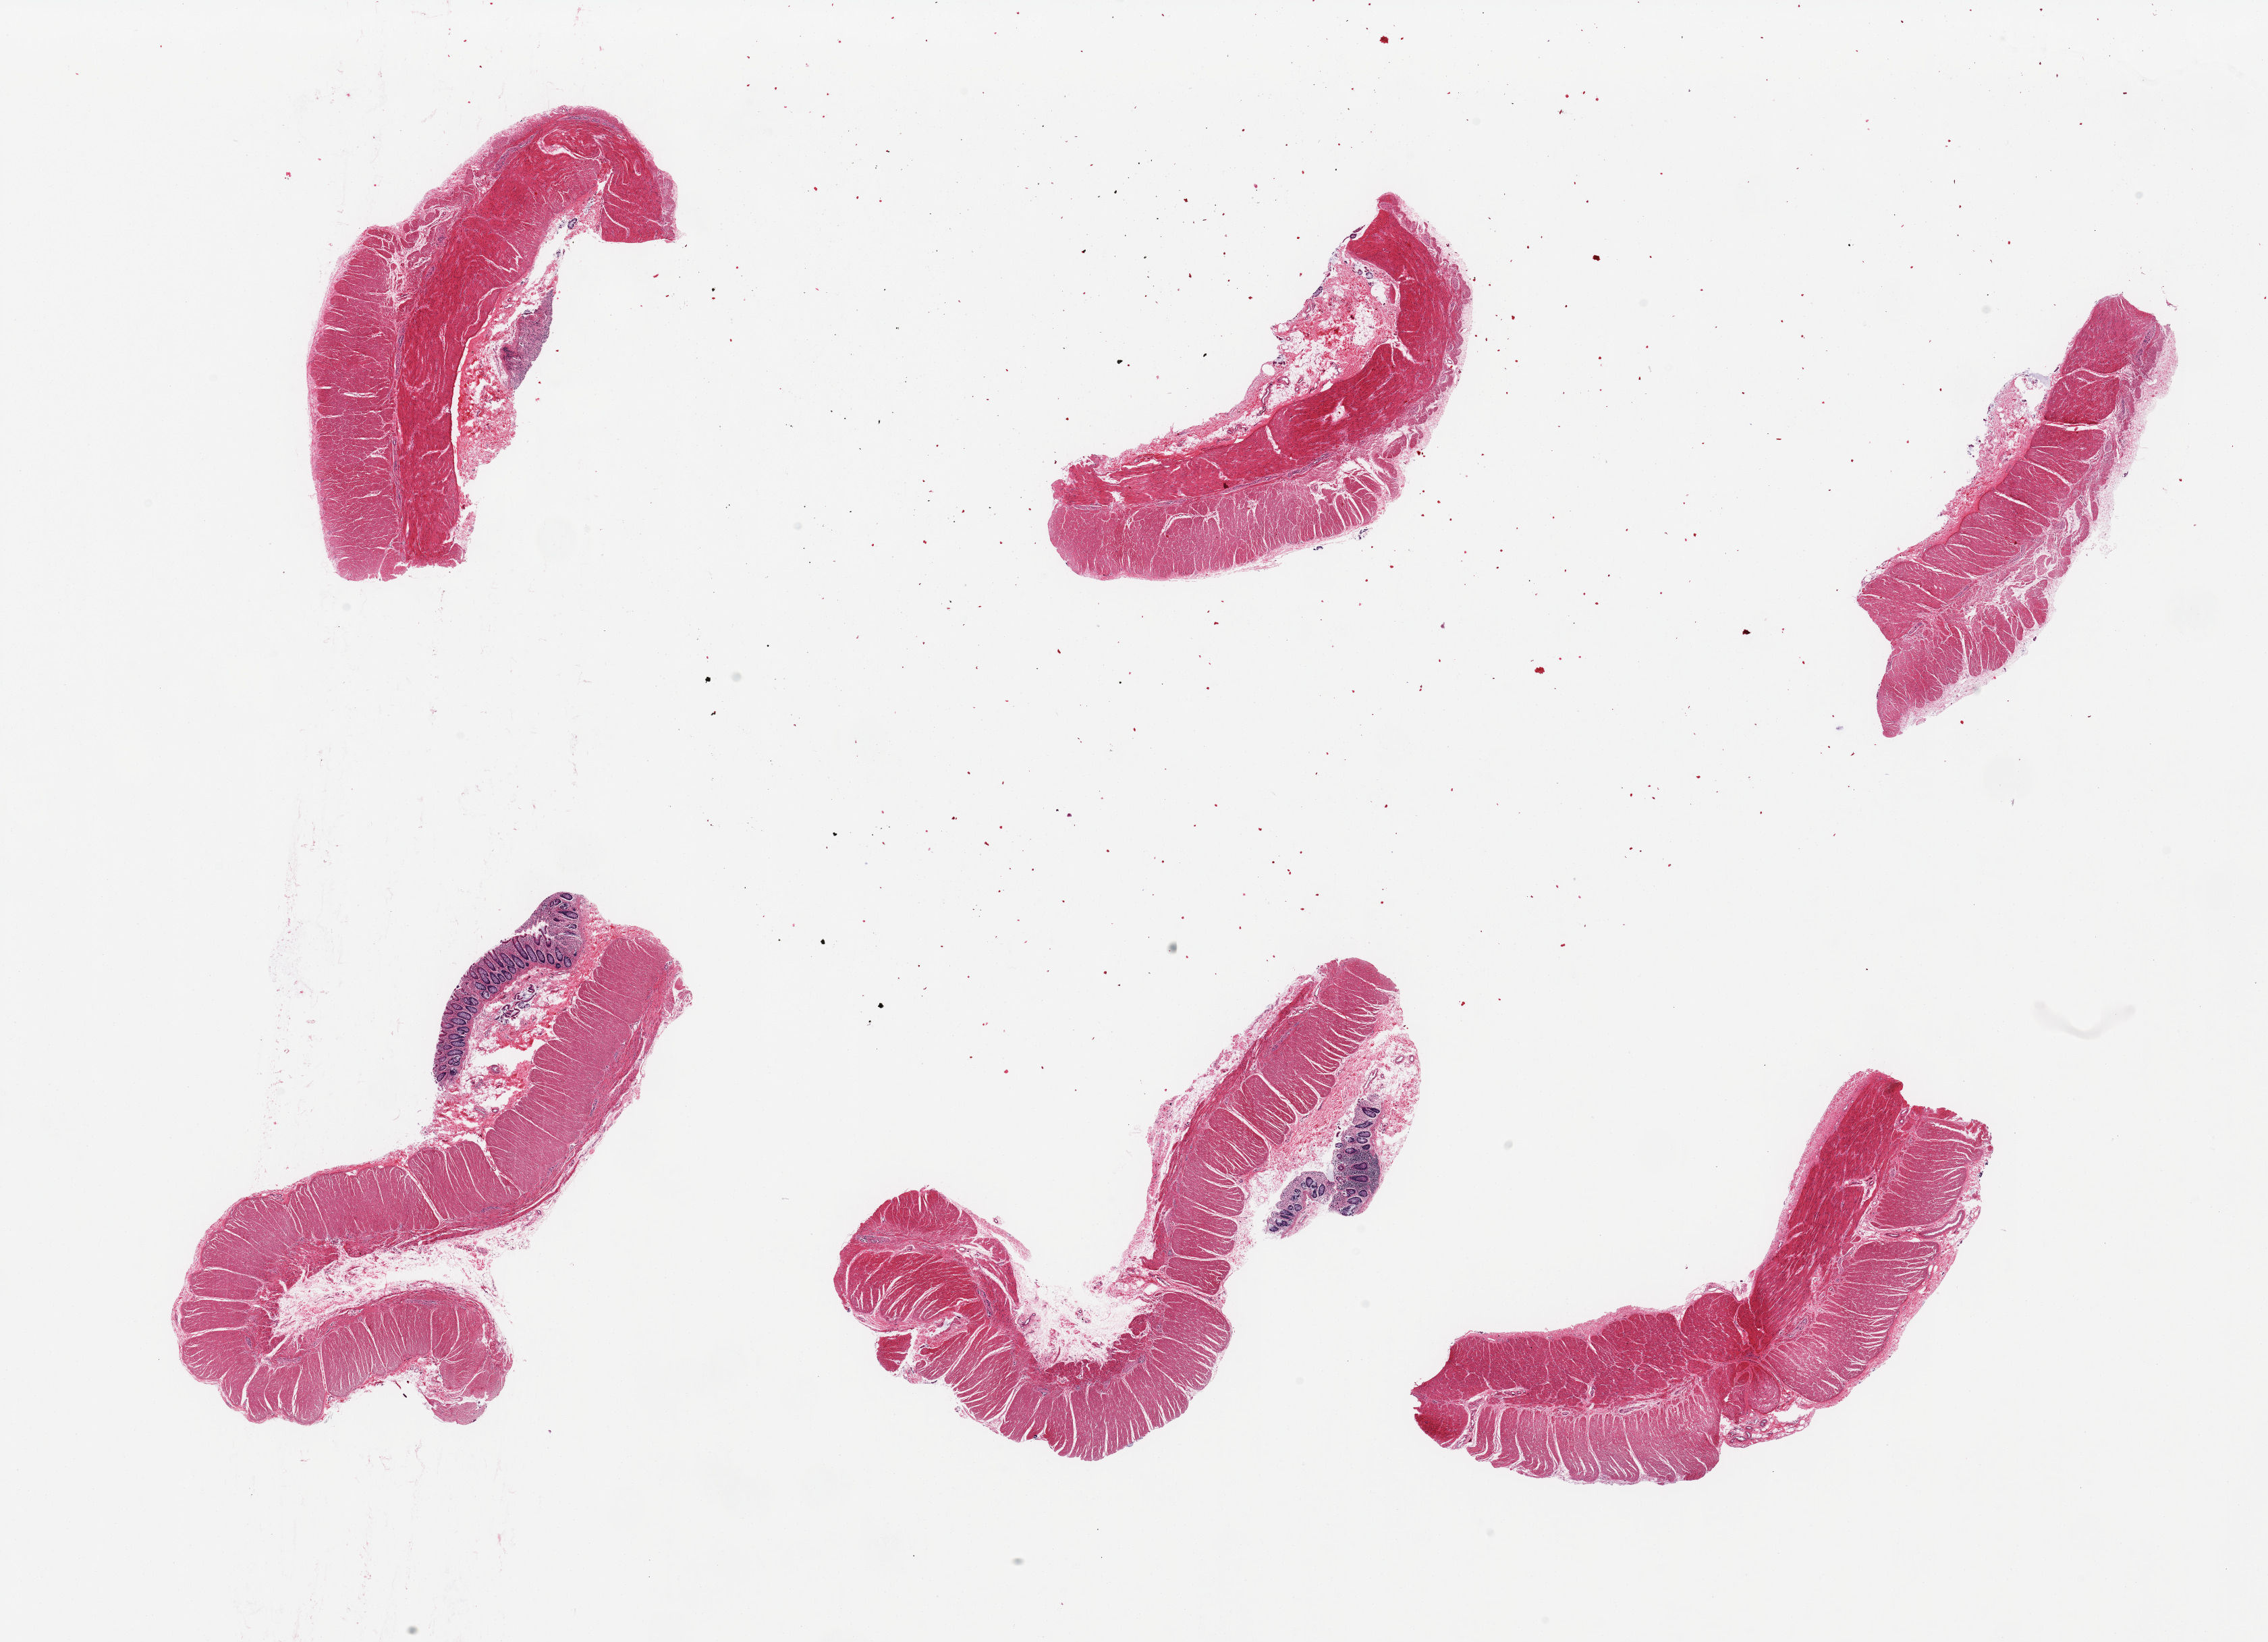
Haematoxylin and eosin whole-slide image, low-resolution overview of the scanned area, about 26.6 x 19.2 mm (acquisition: 20x scan), PAXgene-fixed paraffin-embedded (PFPE) section, sampled site (target tissue): sigmoid colon, donor tissue sample. Donor sex: male.
- reviewer comment on this tissue sample: 6 pieces; 2 pieces have mucosa attached, 2 and 2.5mm long